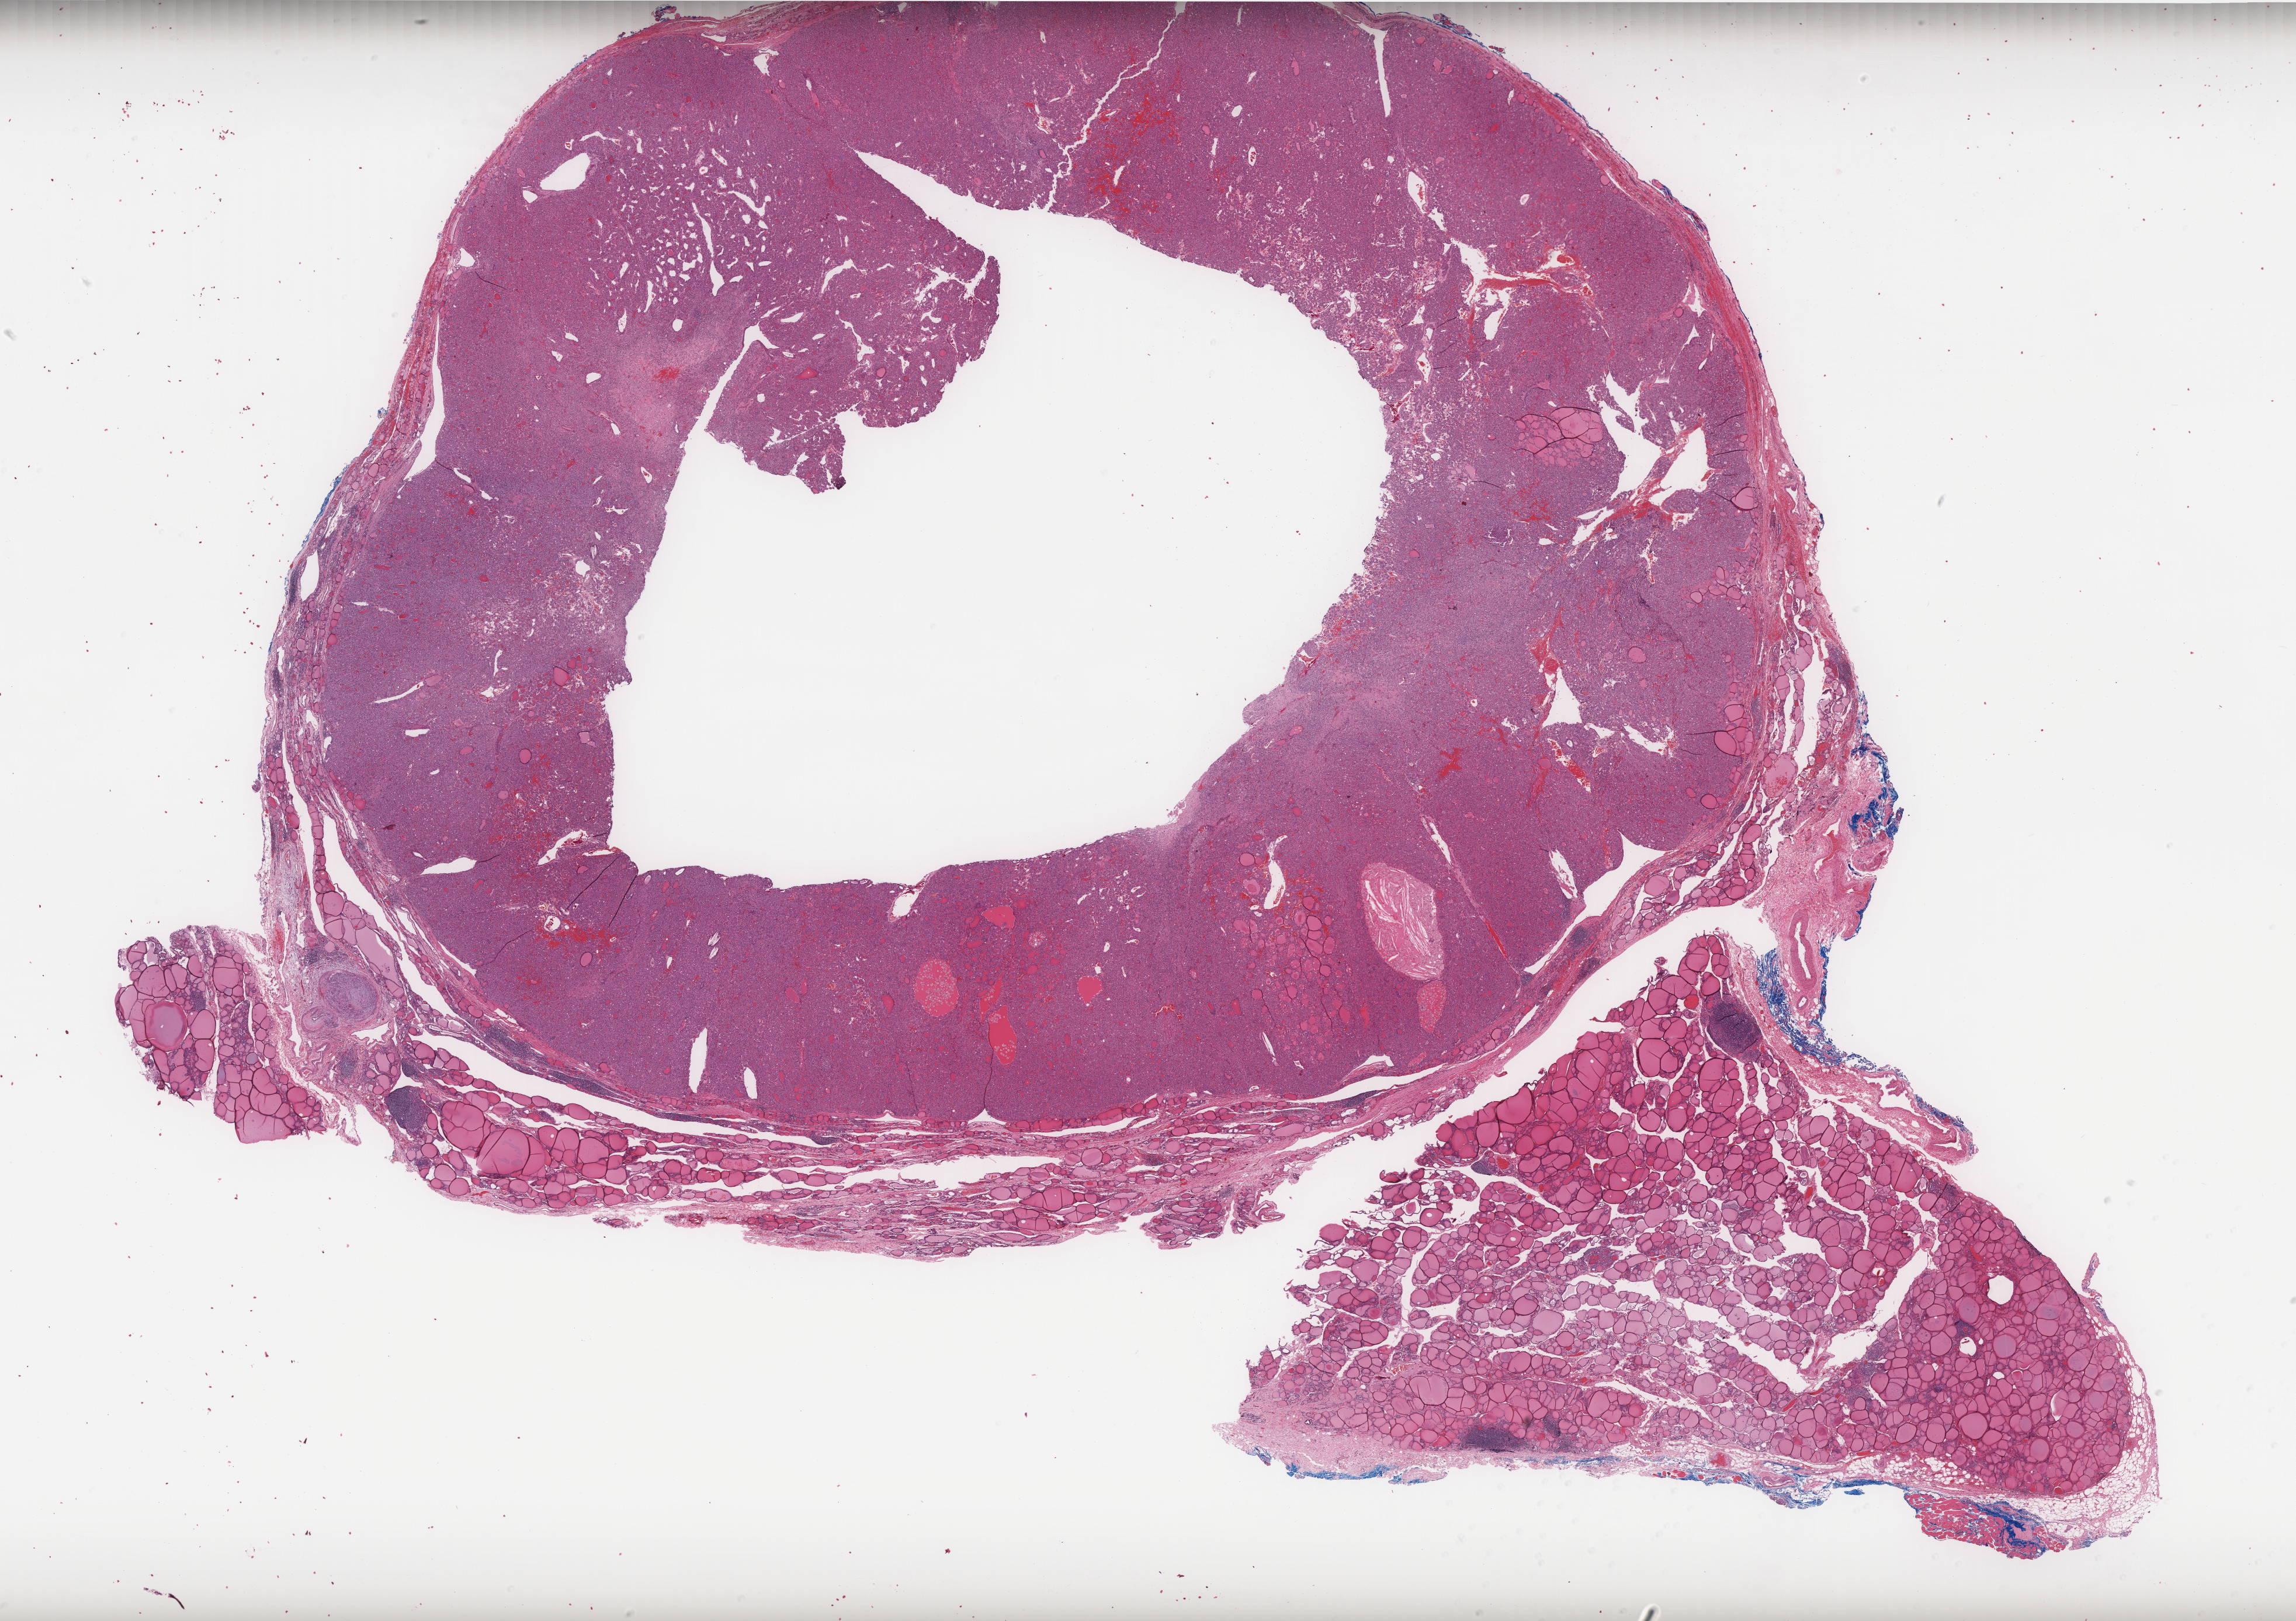
Whole-slide histology image, H&E-stained — low-resolution overview of the scanned area, about 31.5 x 22.2 mm; formalin-fixed paraffin-embedded (FFPE) diagnostic section; primary tumour sample from the thyroid. Female patient; age at initial diagnosis 54 years.
* TNM: T2 N0 M0
* AJCC pathologic stage: II (7th edition)
* histologic diagnosis: Follicular carcinoma, minimally invasive (thyroid gland)